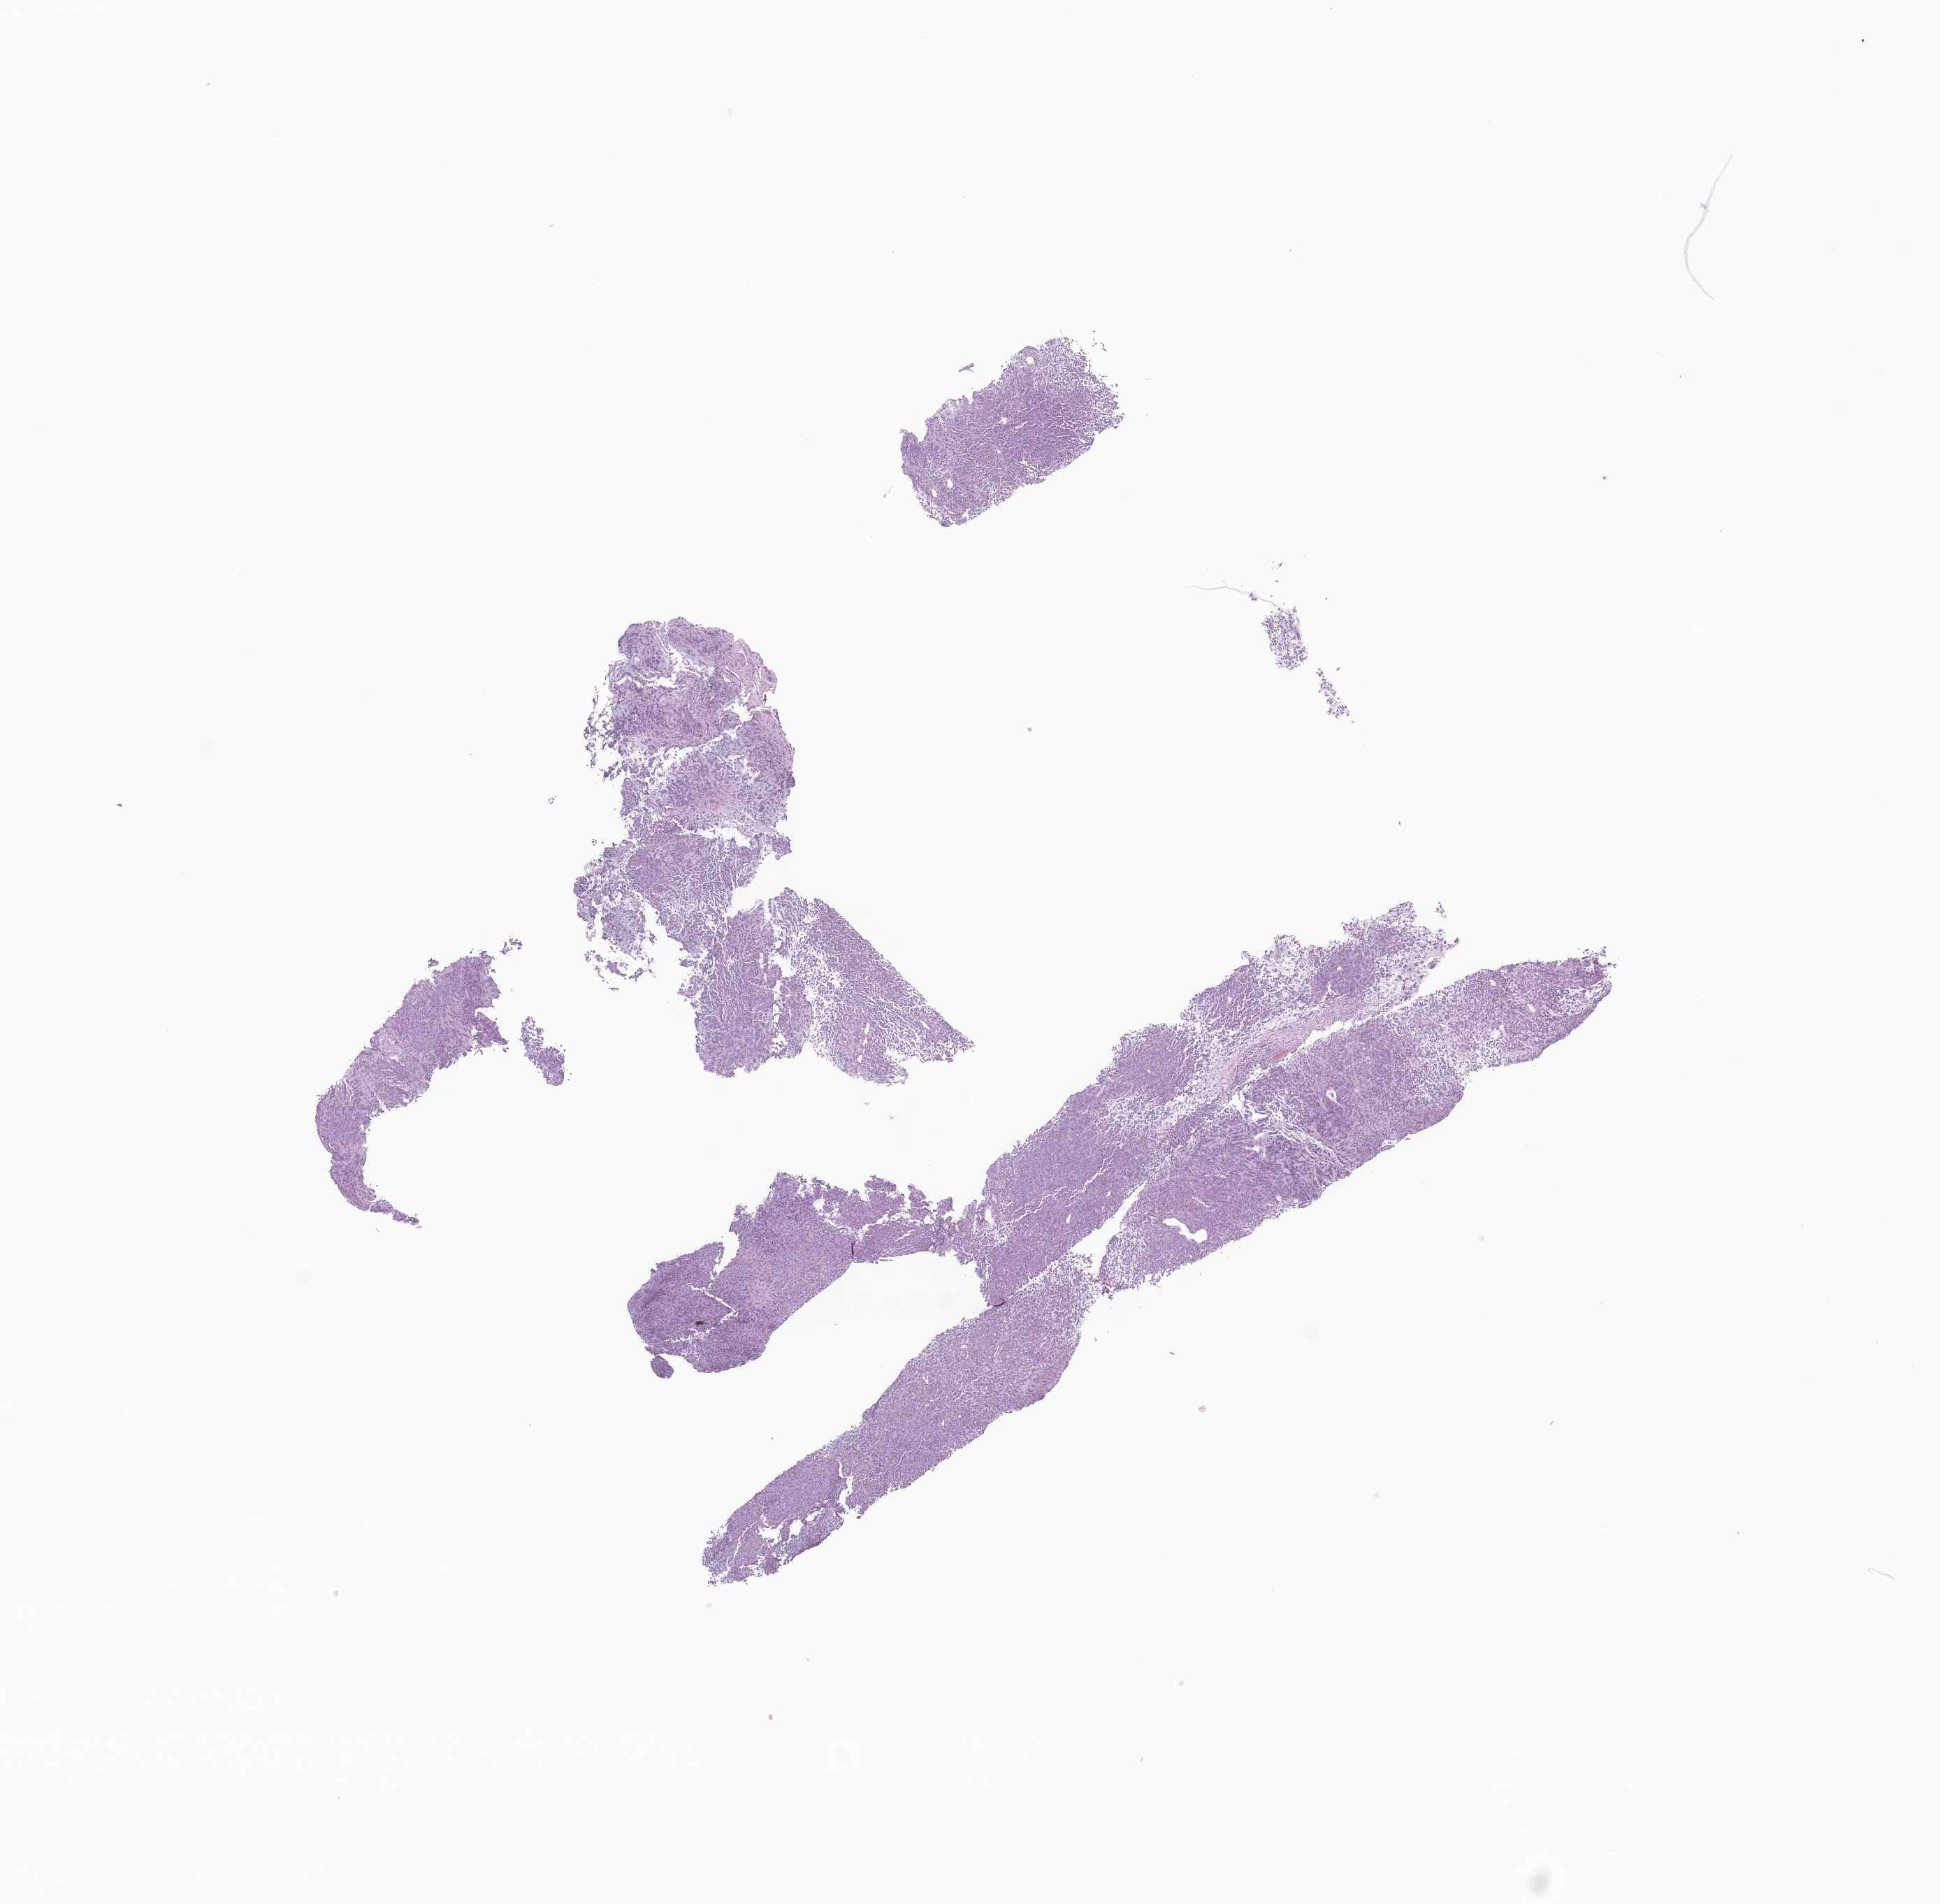
Whole-slide image, H&E stain of tumor tissue from the head and neck, a low-resolution overview of the entire scanned area, about 11.7 x 11.5 mm; FFPE section. Male patient, age 174 days.
Diagnosis: Rhabdoid tumor, NOS.